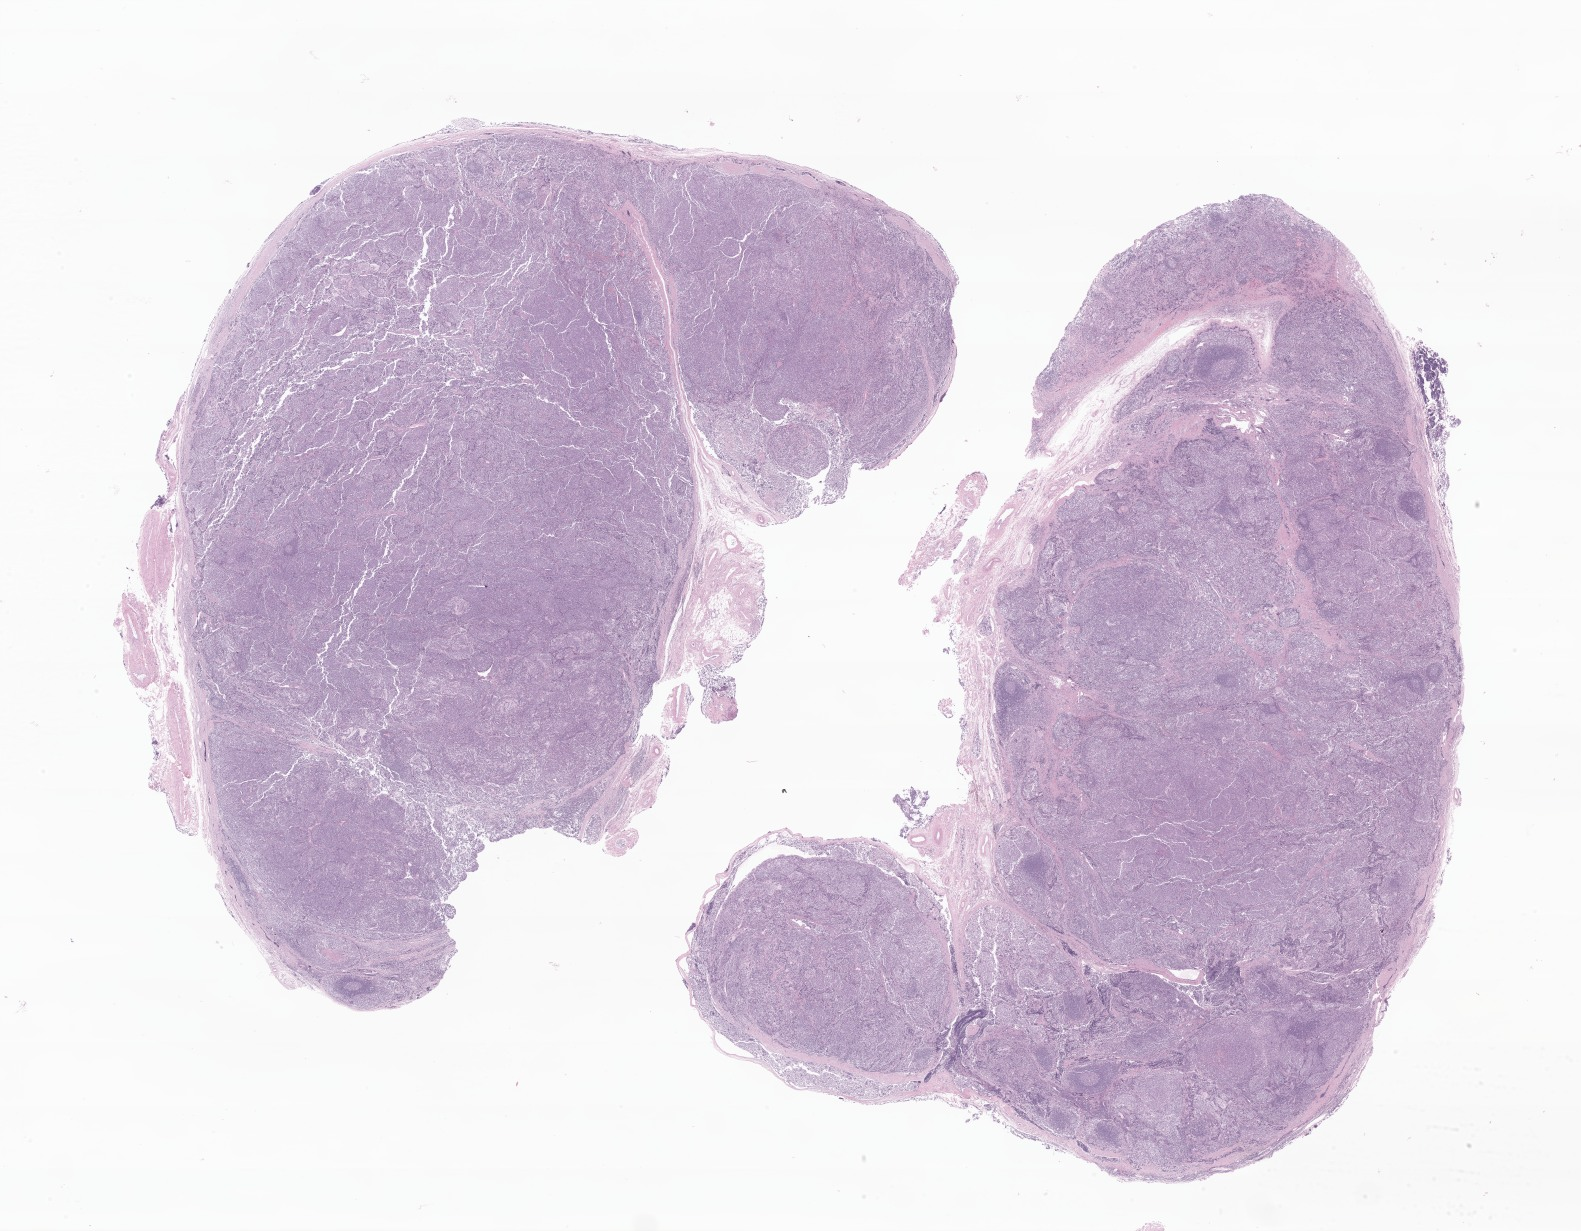
Digitized haematoxylin and eosin-stained section of tumor tissue from the head and neck lymph node, low-resolution overview of the scanned area, about 26.7 x 20.8 mm; FFPE section. Patient: female, age 56 months (4 years 8 months).
* diagnosis (ICD-O-3 morphology term): Neuroblastoma, NOS